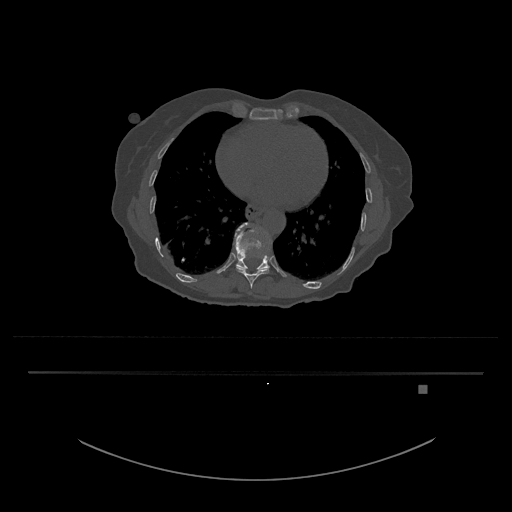
CT including the spine, one axial slice. Slice 694 of 797 in the series (ordered by position). Reconstruction kernel Br40s/3. 120 kVp. Bone window (W 1800 / L 400 HU). 512 × 512 image matrix. Patient: female, 57 years. From the clinical record (not read from this slice): primary cancer: cervical.
Structures marked on this image (semi-automatic segmentation, software-assisted and operator-edited):
- T10 vertebra: bounding box [x1, y1, x2, y2] px = [236, 268, 269, 289]
- T11 vertebra: [233, 222, 272, 270]